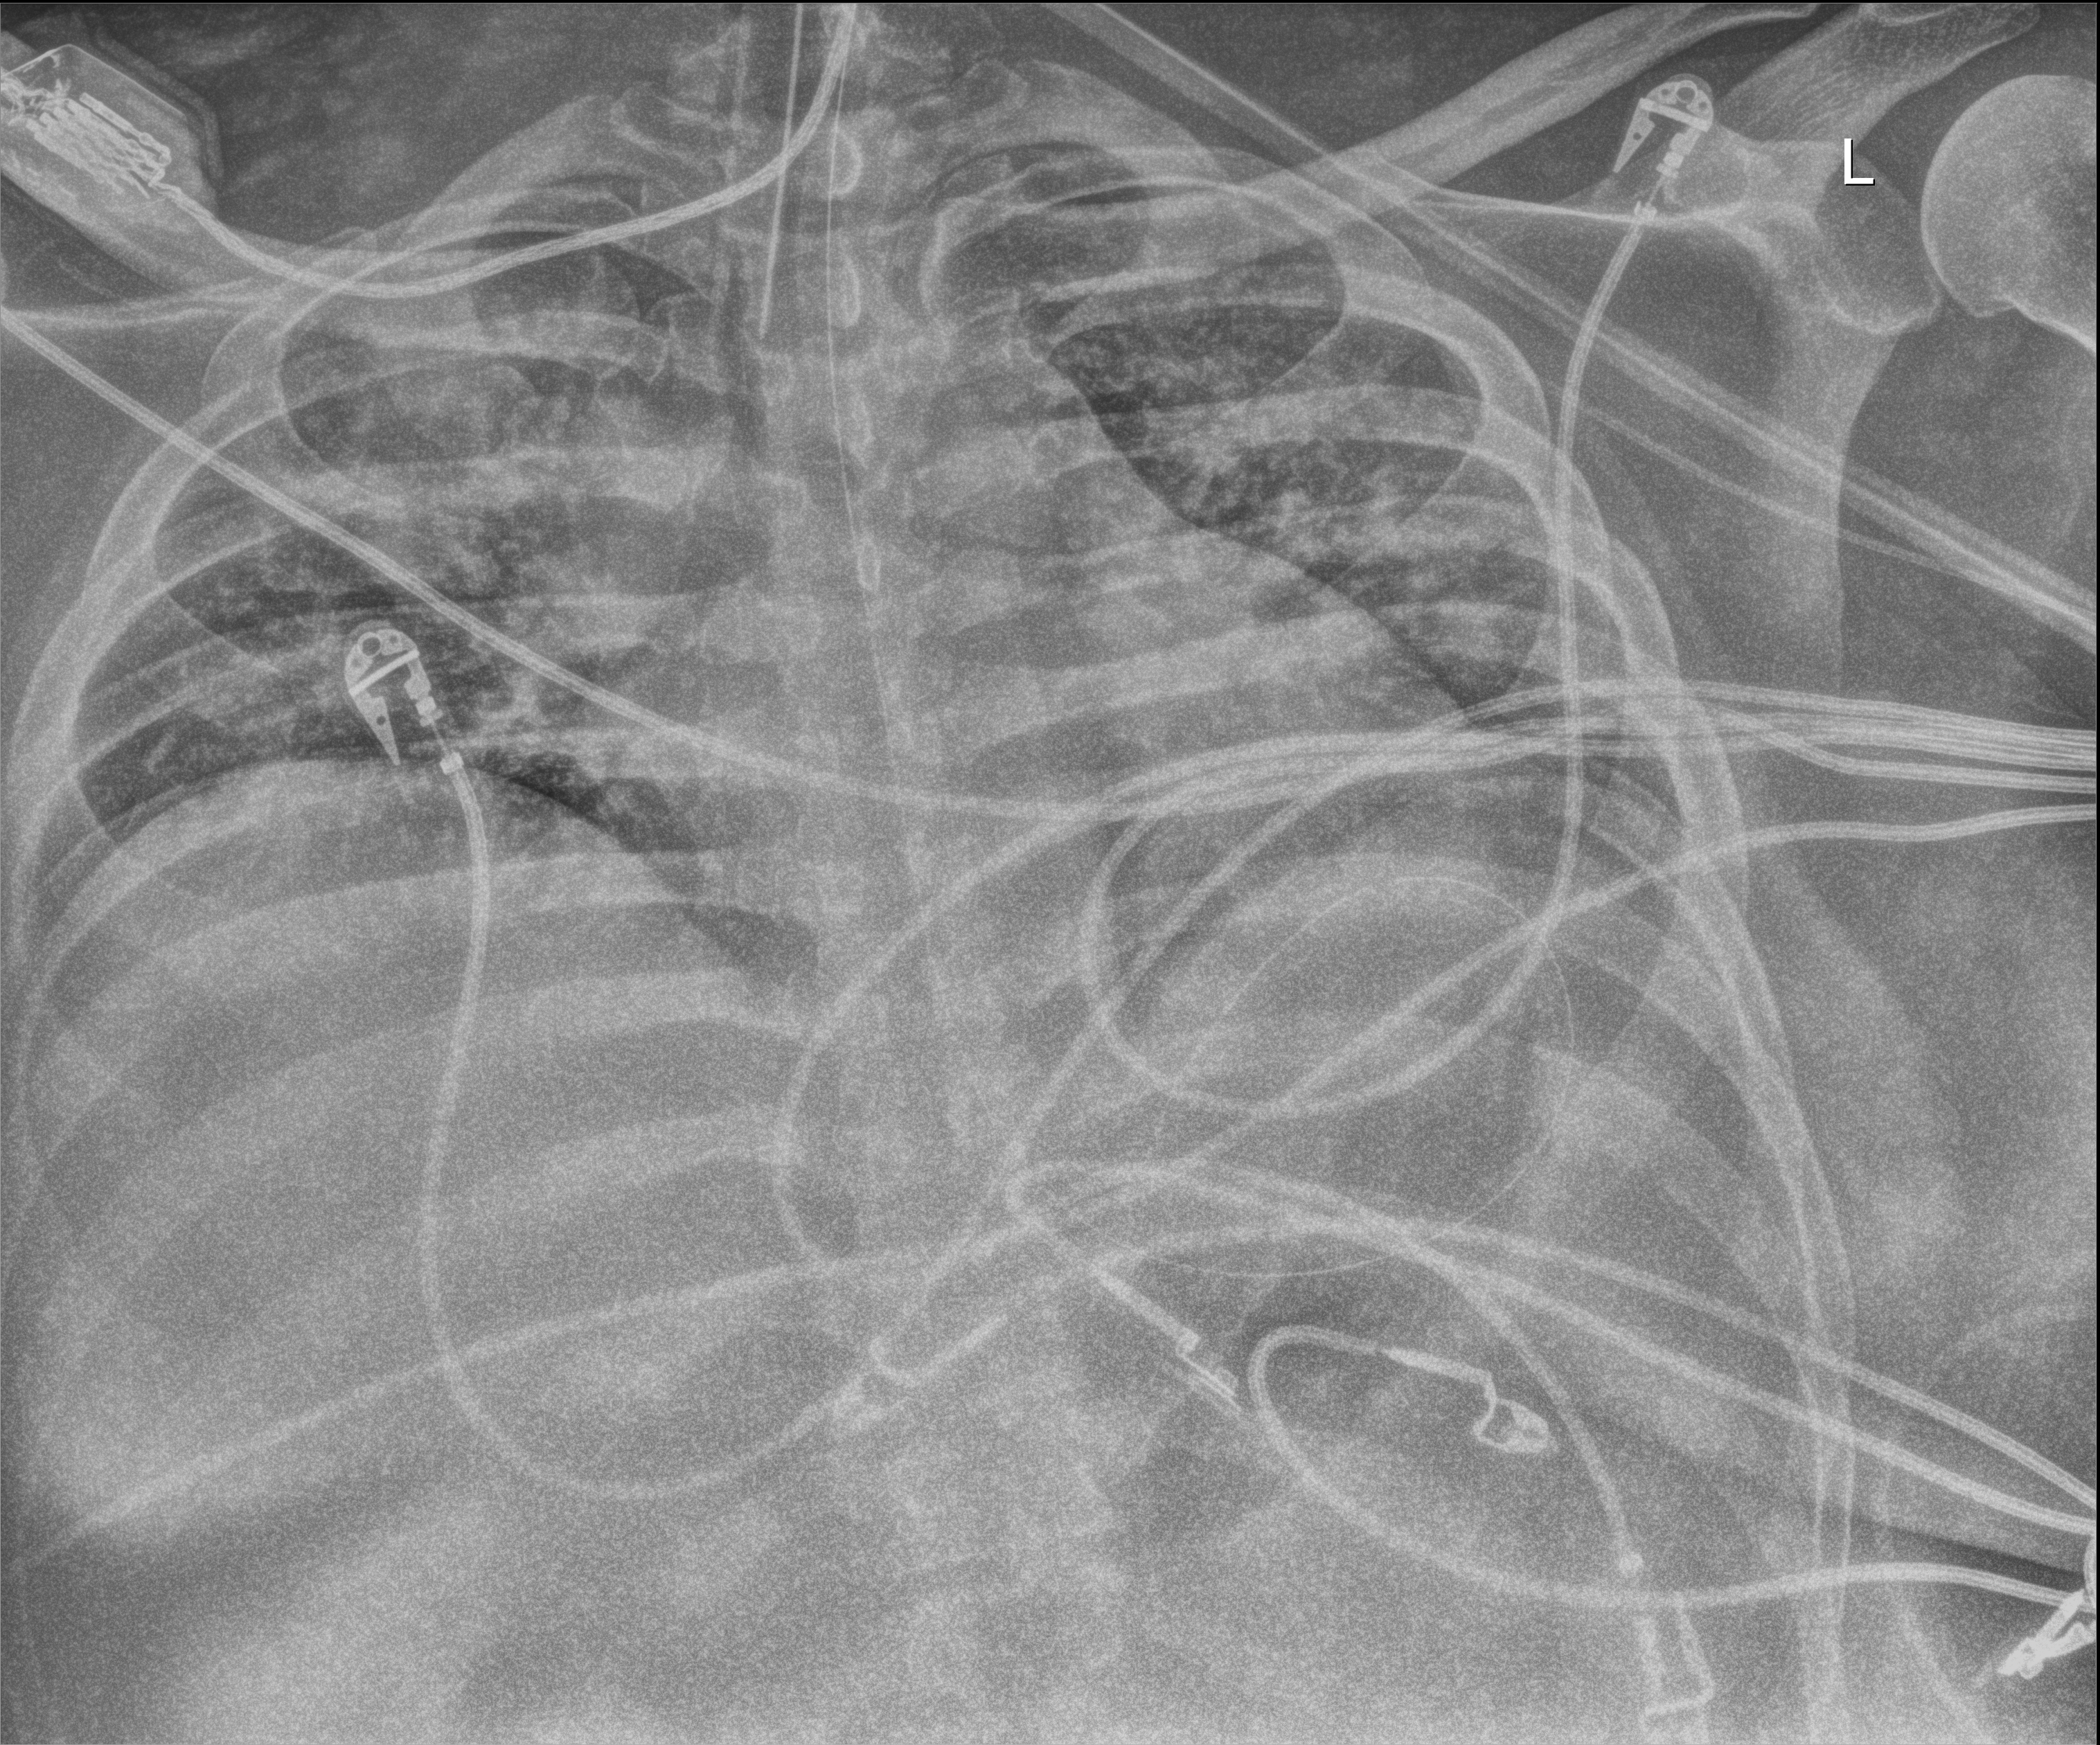
Chest X-ray (portable). Male patient hospitalised with COVID-19, age 18–59 years.
Hospital-stay facts (about this admission, not read from this image; timing relative to this image not recorded): COPD (admission record): yes.